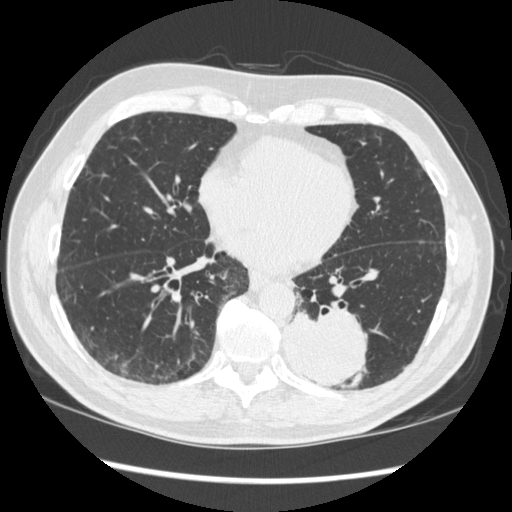
Low-dose screening chest CT, one axial slice. Reconstruction kernel STANDARD. 120 kVp. Lung window (W 1500 / L -600 HU). 512 × 512 image matrix.
Outlined on this slice (manually delineated by an expert):
- lesion 1 (tumor, lower lobe of left lung): bounding box (x1, y1, x2, y2) in pixels: (284, 311, 368, 389)